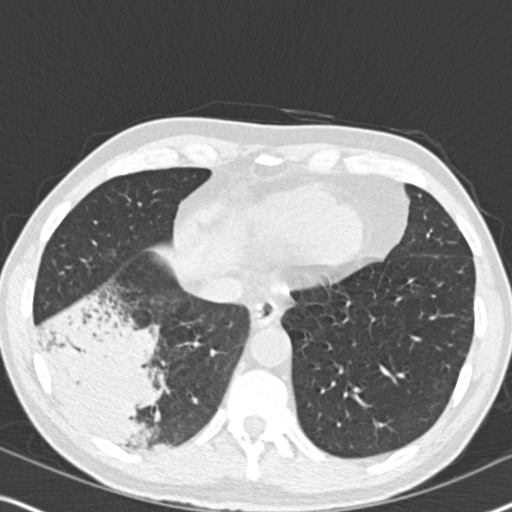
Low-dose screening chest CT, one axial slice; slice 61 of 182 in the series (ordered by position); lung window (W 1500 / L -600 HU); 2 mm slice thickness; 512 × 512 image matrix, field of view 330 × 330 mm.
Annotated regions visible in this slice (manually delineated by an expert):
- lesion 1 (tumor, lower lobe of right lung): box from (x=43, y=314) to (x=153, y=447) px